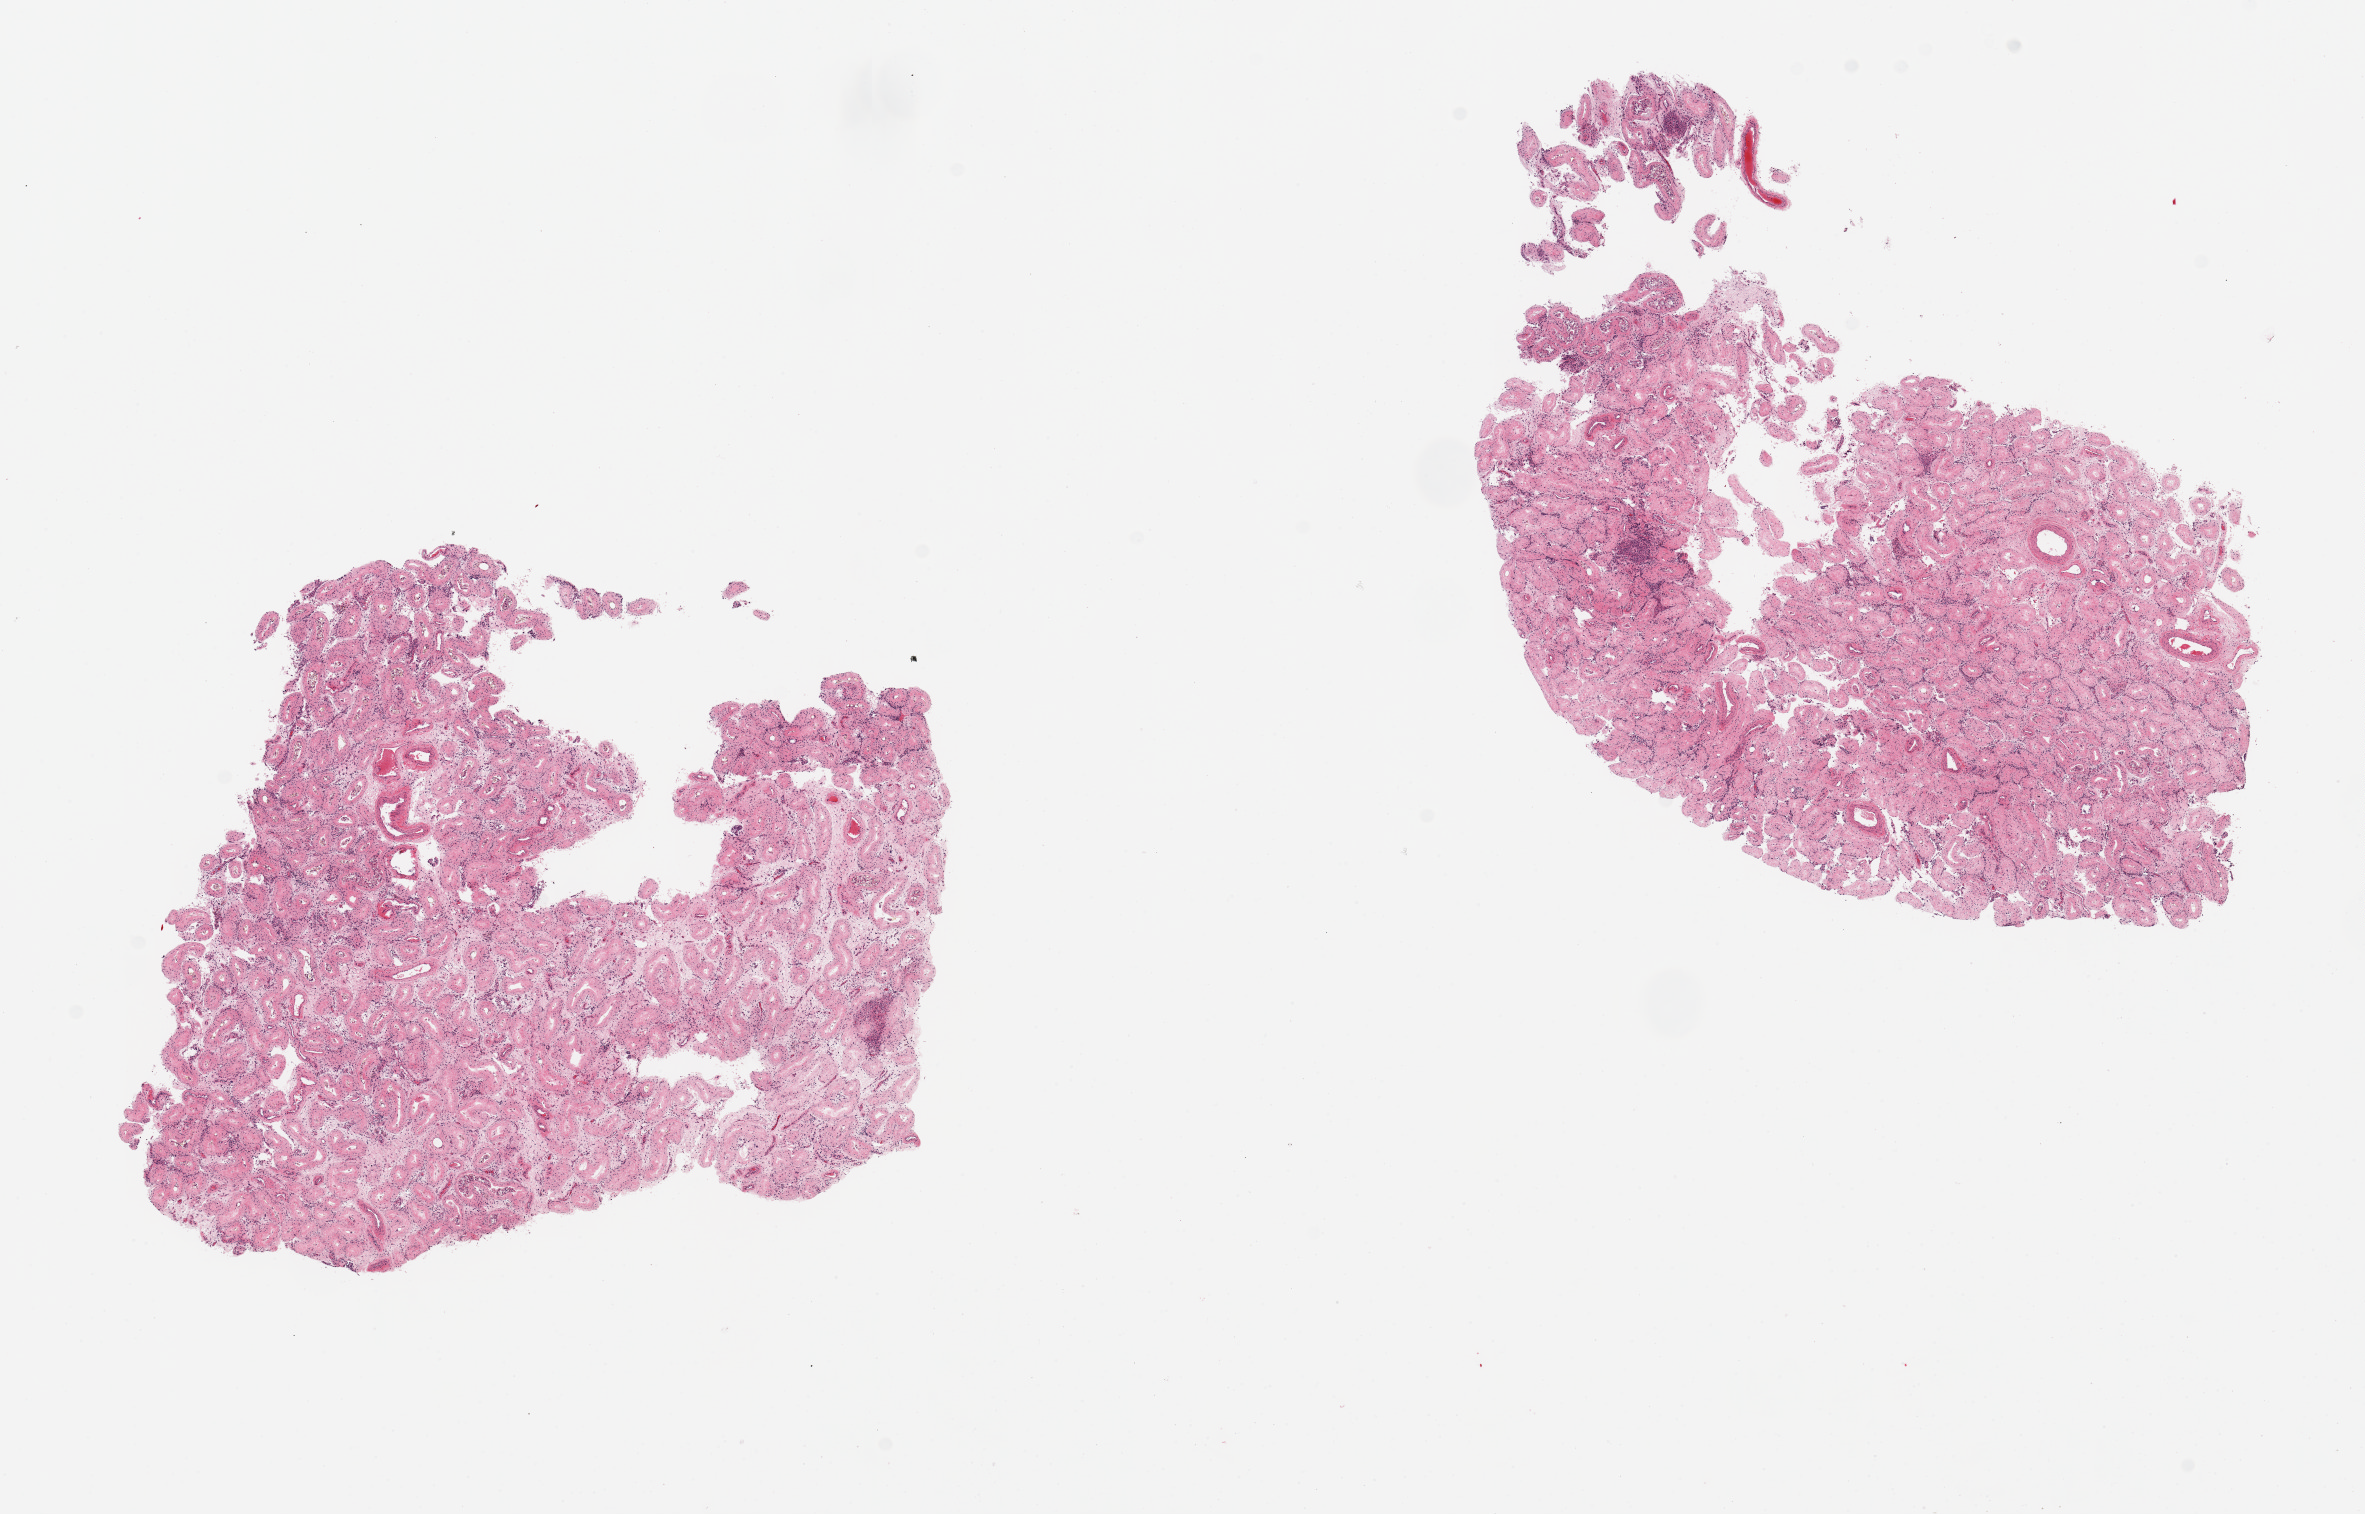
Hematoxylin and eosin (H&E) whole-slide image — shown as a low-resolution overview of the whole scanned area (about 18.7 x 12.0 mm, acquisition: 20x scan); PAXgene-fixed, paraffin-embedded tissue; sampled site (target tissue): testis; tissue donor sample. Male donor.
Reviewer comment on this tissue sample: 2 pieces; sclerosis/ atrophy of seminiferous tubules, no significant Leydig cell hyperlasia, c/w history of cirrhosis.